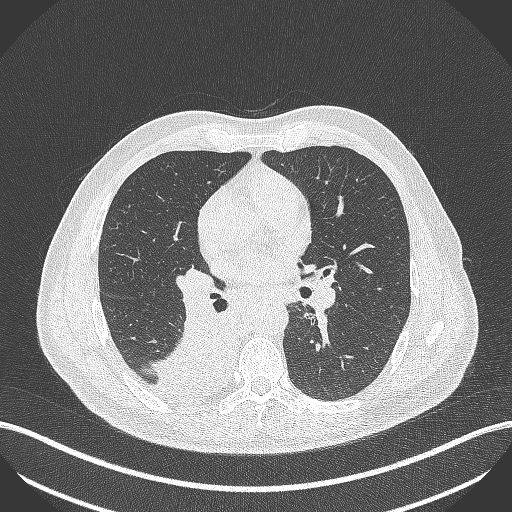
Chest CT, one axial slice; slice 254 of 451 in the series (ordered by position); reconstruction kernel B70f; 100 kVp; lung window (W 1500 / L -600 HU); 1 mm slice thickness; 512 × 512 image matrix, field of view 400 × 400 mm. Male patient, age 61 years. From the clinical record (not read from this slice): clinical TNM (as recorded): T1 N0 M0.
Structures marked on this image (rectangle marked by the reading radiologist):
- lung tumour (recorded histology: small cell carcinoma): bounding box <143,314,234,400> (left, top, right, bottom; pixels)